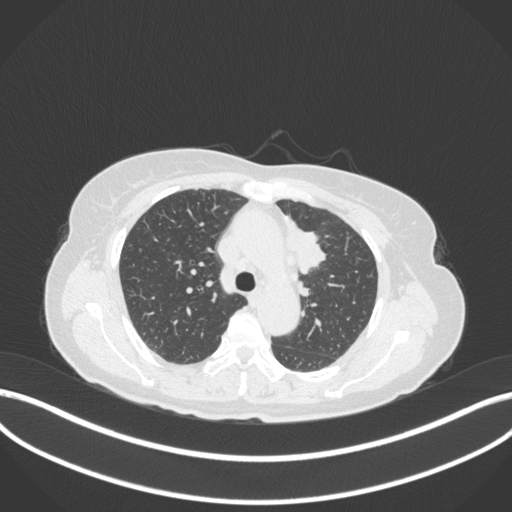
Chest CT, one axial slice. Position 235 of 368 along the scan axis. Reconstruction kernel B31f. 120 kVp. Lung window (W 1500 / L -600 HU). 1 mm slice thickness. 512 × 512 image matrix. Patient: female, 65 years. From the clinical record (not read from this slice): clinical TNM (as recorded): T2a N0 M0.
Annotated regions visible in this slice (bounding box drawn by a radiologist):
- lung tumour (recorded histology: adenocarcinoma): bounding box (x1, y1, x2, y2) in pixels: (278, 213, 329, 275)